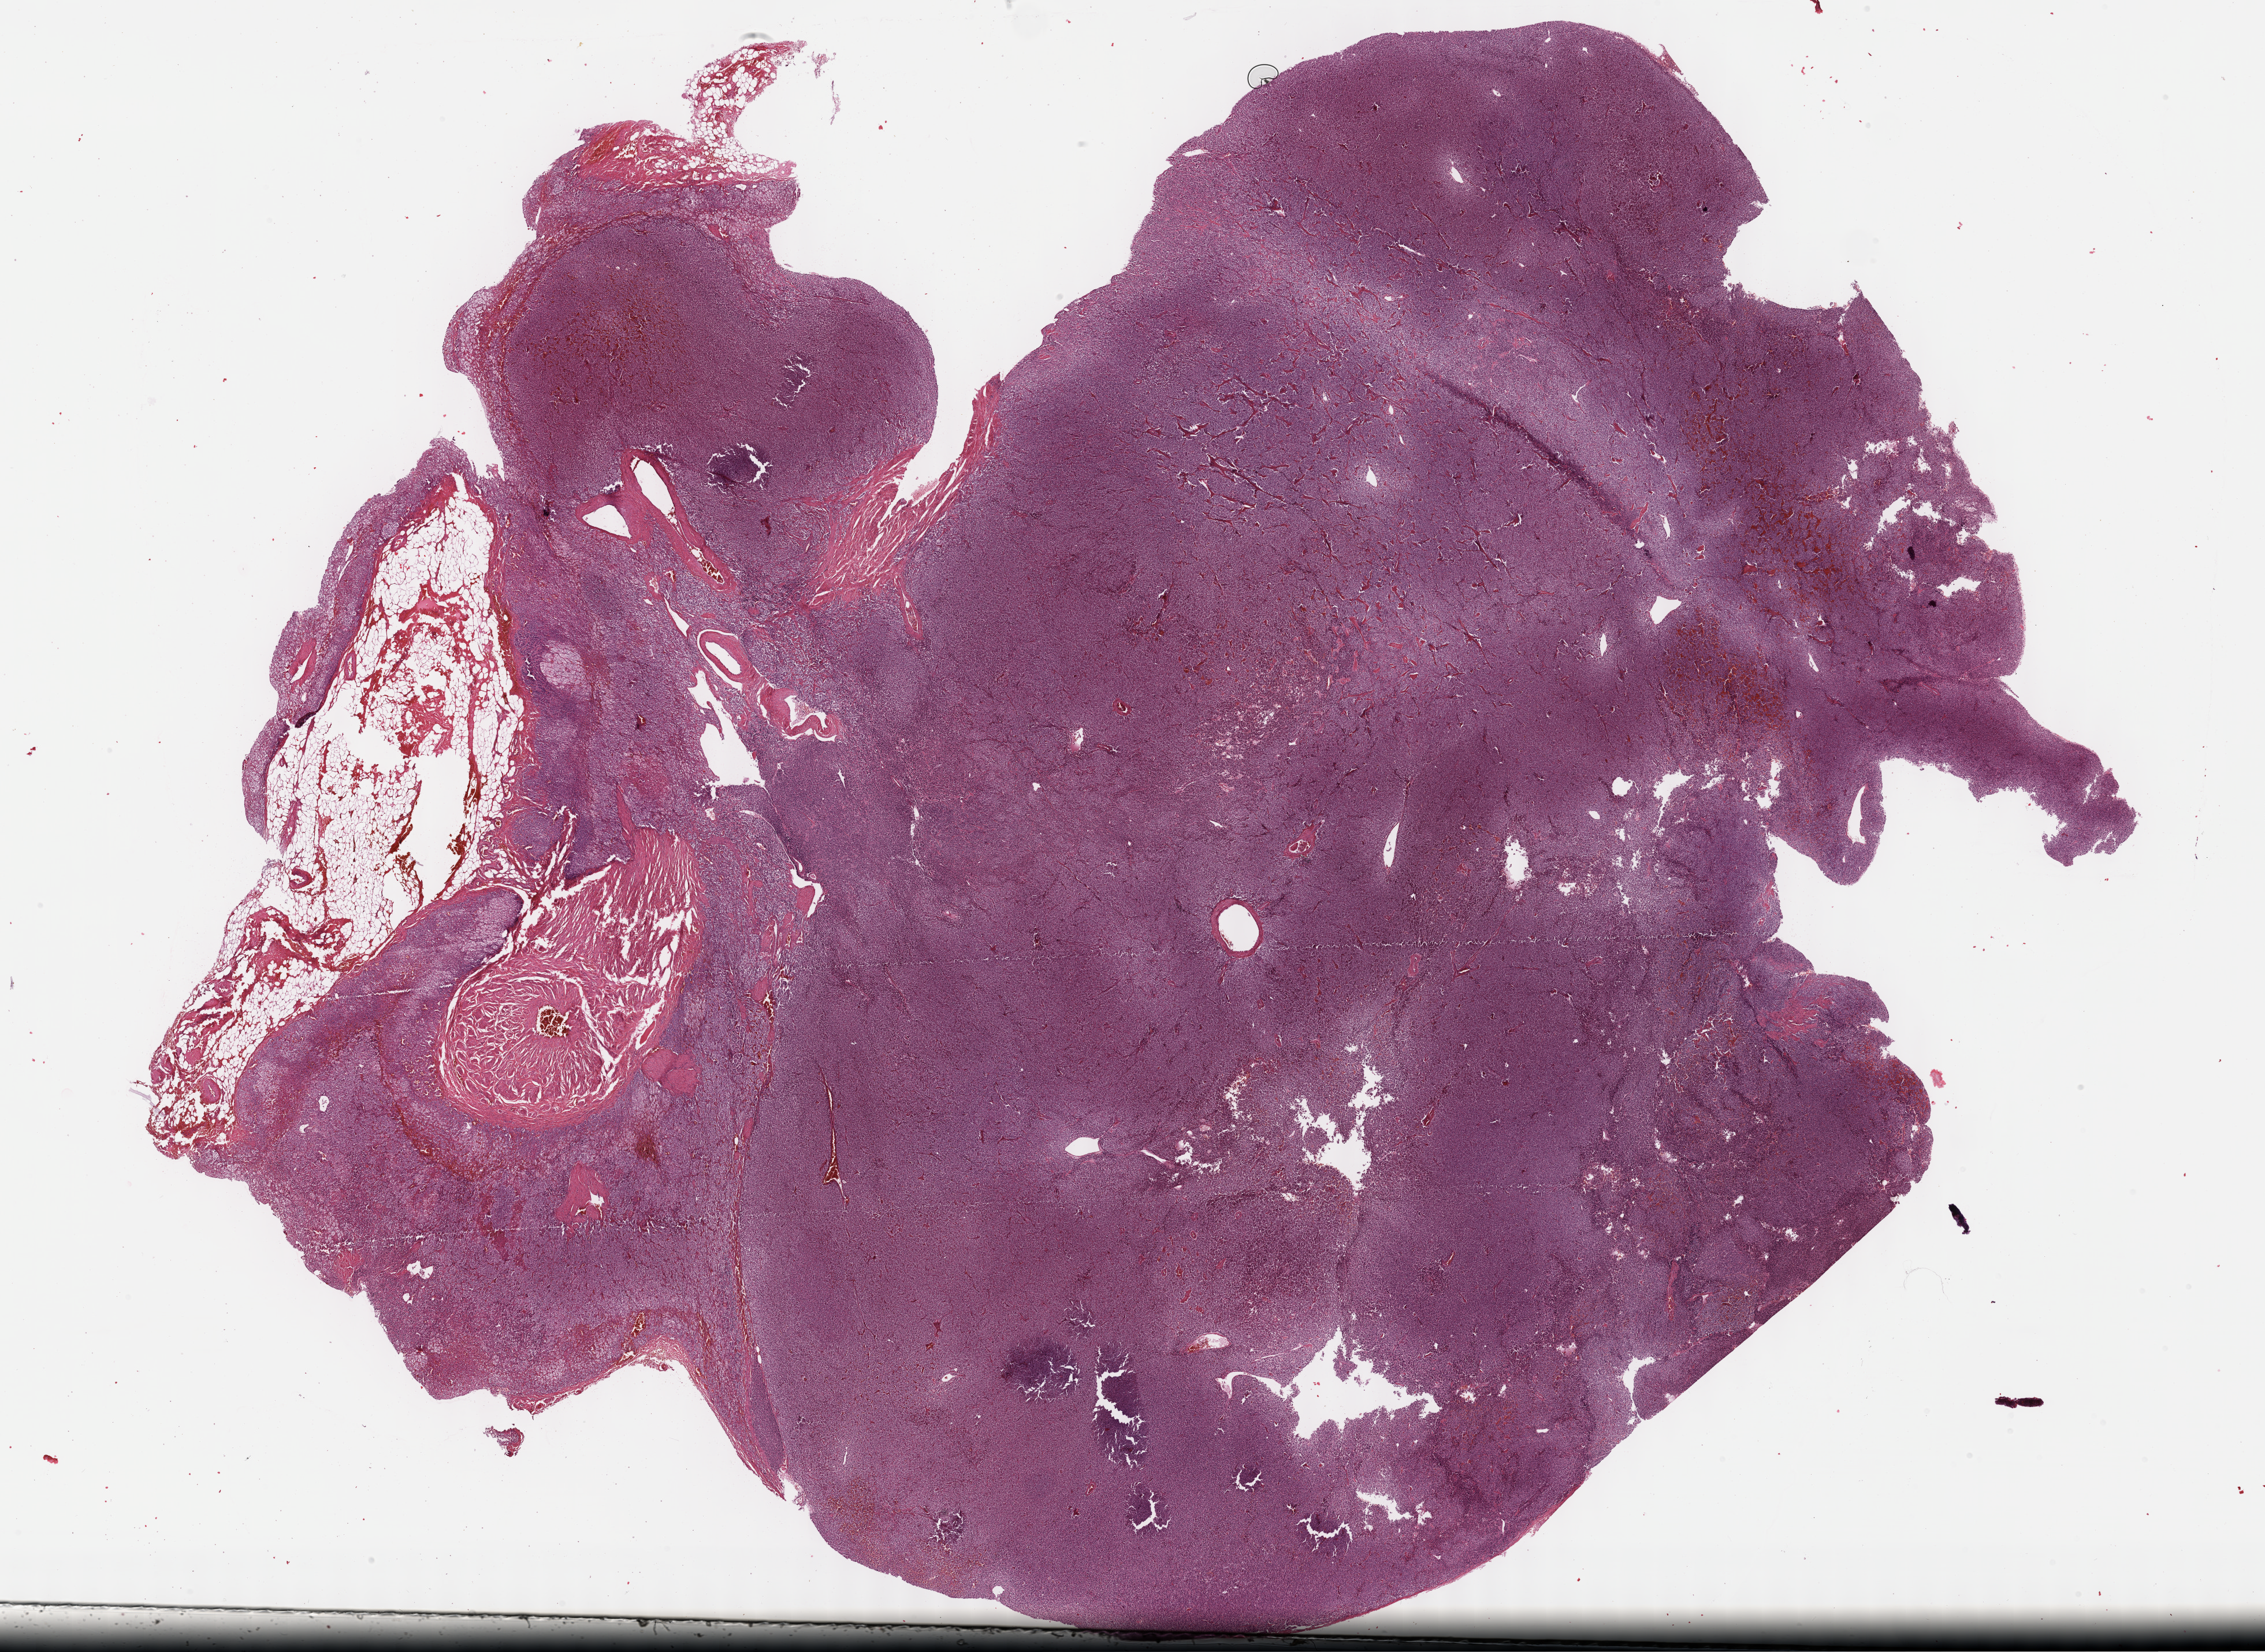
Digitized Hematoxylin and eosin (H&E) stained tissue section (whole slide) — whole scanned area (about 31.7 x 23.1 mm, from a 40x scan) shown as a low-resolution overview. Formalin-fixed paraffin-embedded (FFPE) diagnostic section. Primary tumour sample from the adrenal gland. Patient: female, age at initial diagnosis 63 years.
Laterality: left. Histologic diagnosis: Pheochromocytoma, malignant.